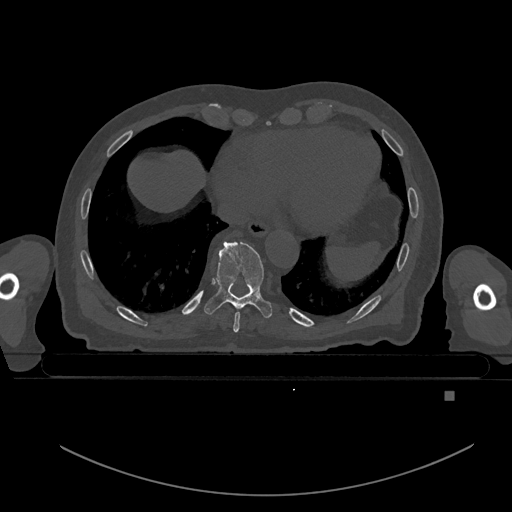
CT including the spine, one axial slice; position 154 of 969 along the scan axis; bone window (W 1800 / L 400 HU); 512 × 512 image matrix, field of view 456 × 456 mm. Patient: male, 82 years. Case-level facts recorded for this patient, not image findings: primary cancer: prostate.
Annotated regions visible in this slice (semi-automatic segmentation, software-assisted and operator-edited):
- T8 vertebra: bounding box [x1, y1, x2, y2] px = [233, 312, 241, 333]
- T9 vertebra: [204, 241, 272, 318]